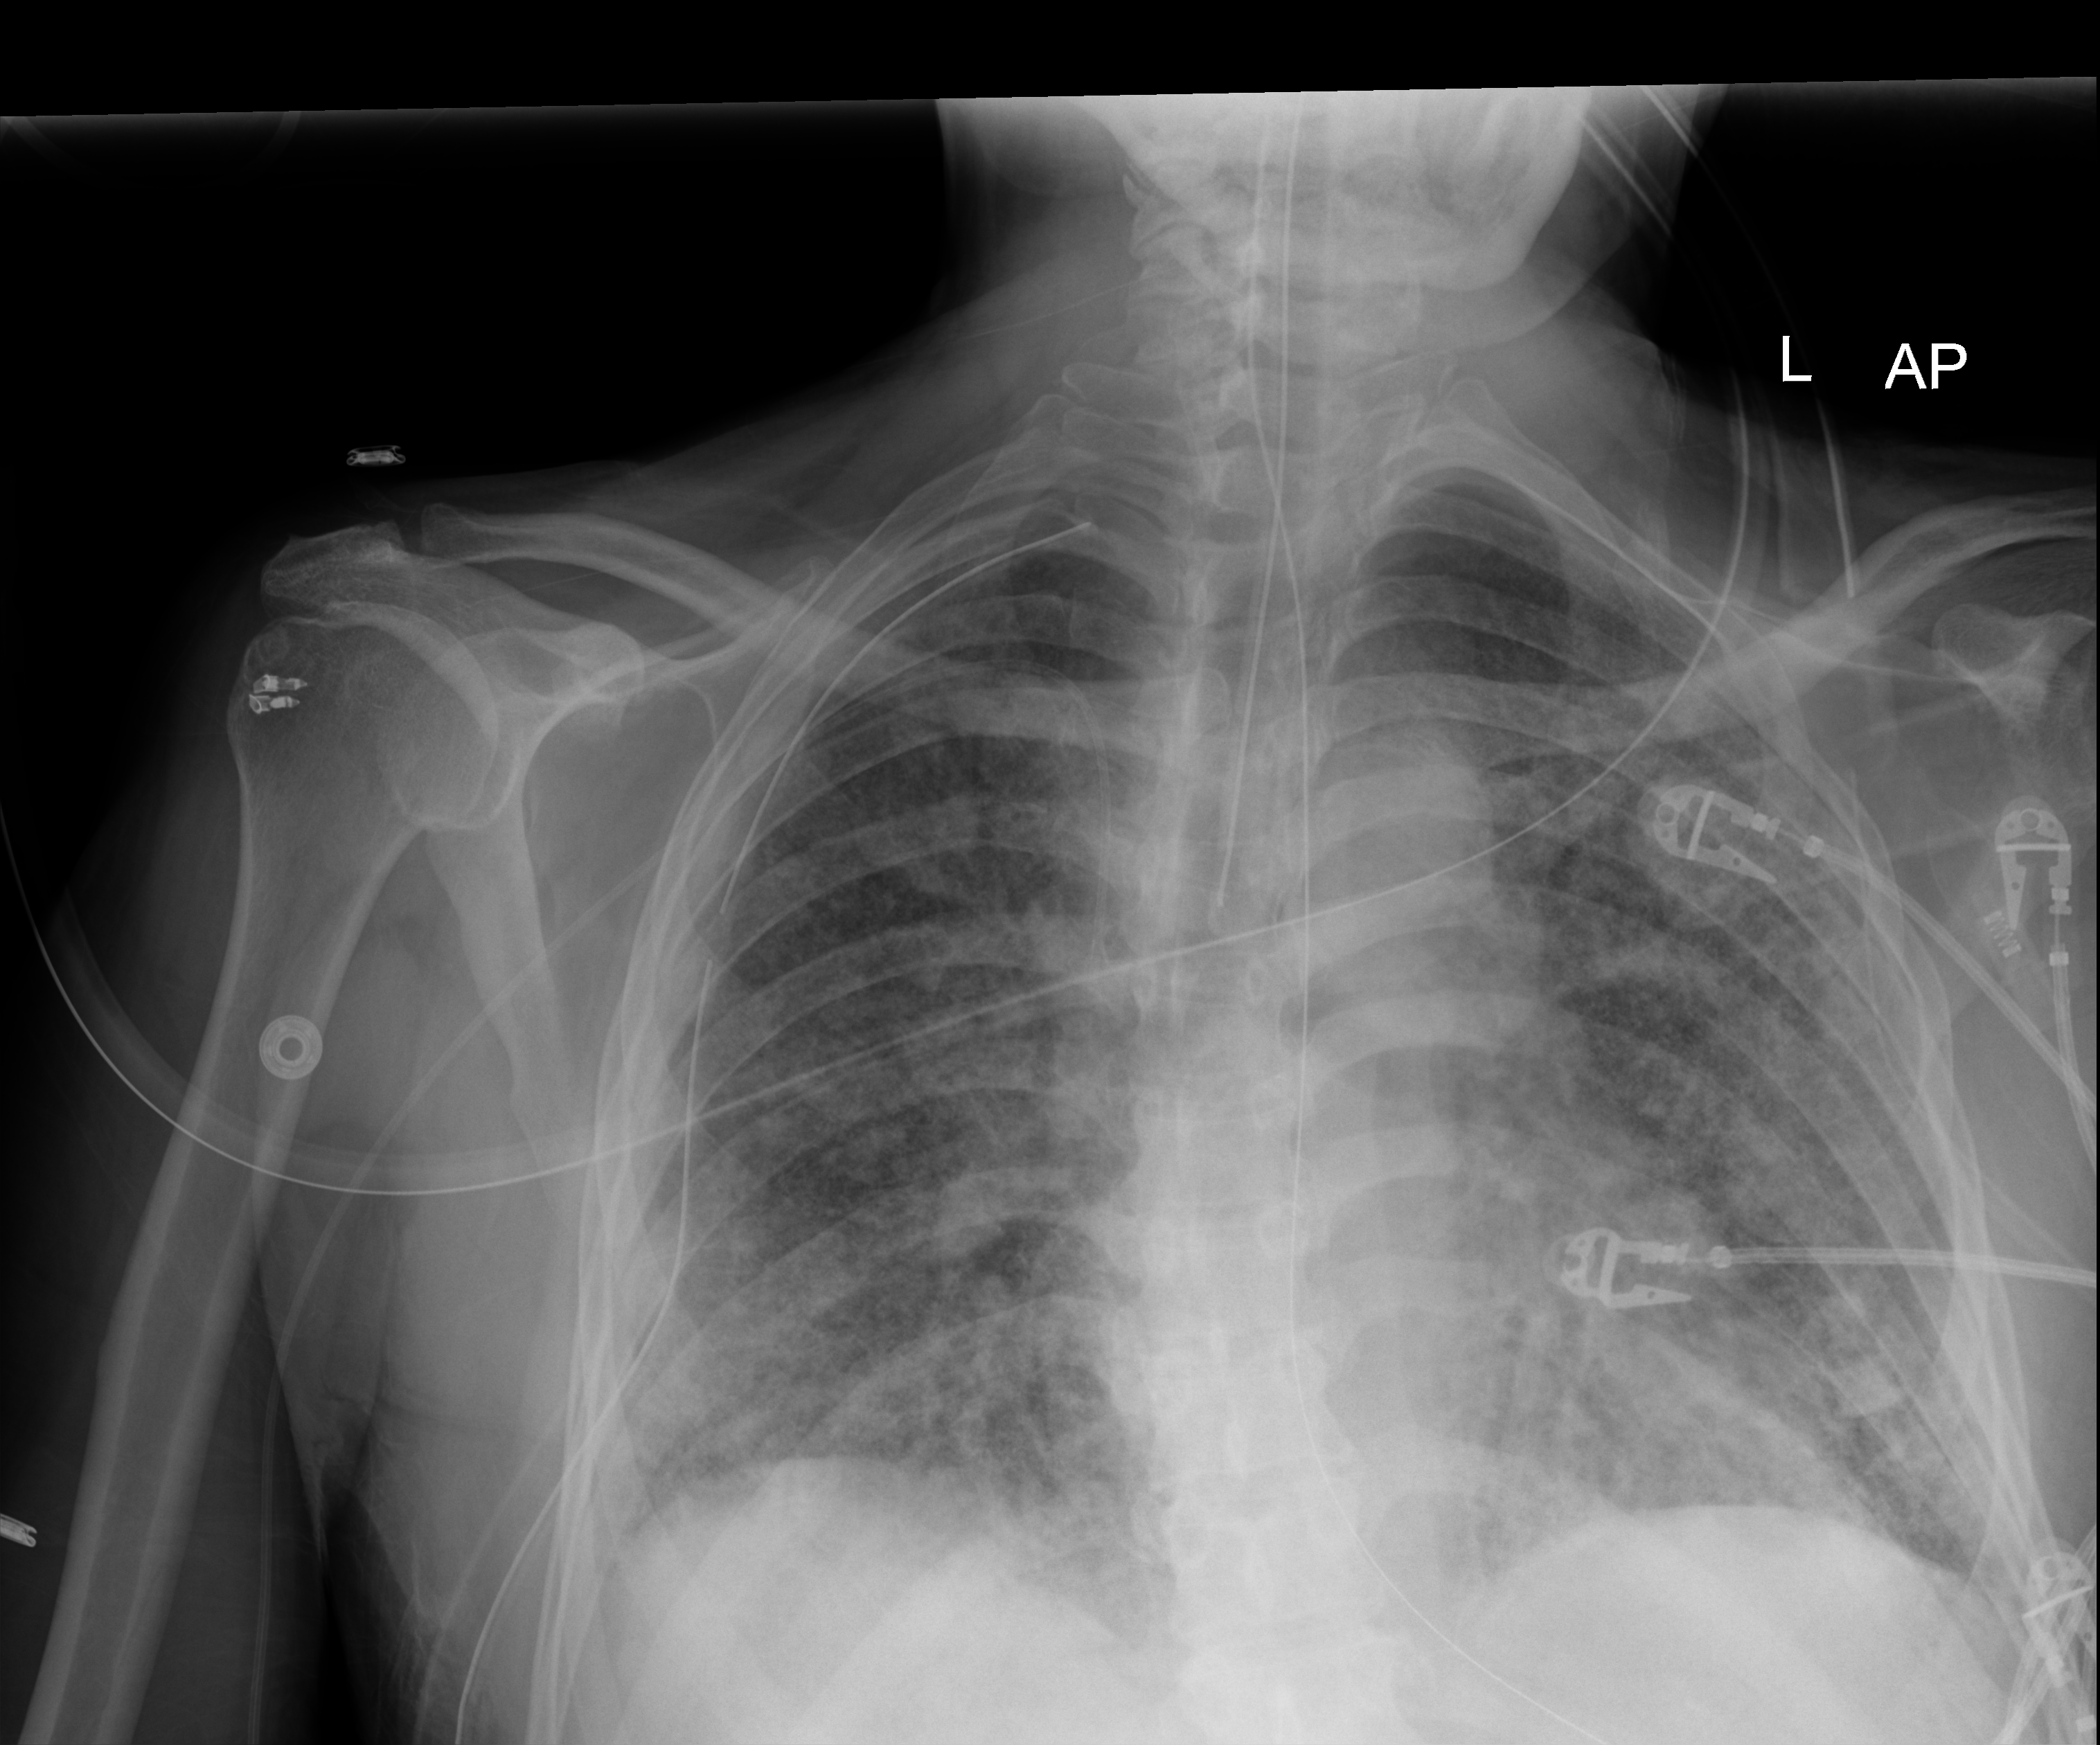
Chest X-ray (portable). Male patient hospitalised with COVID-19, age 60–74 years.
Hospital-stay facts (about this admission, not read from this image; timing relative to this image not recorded): admitted to intensive care during this hospital stay: yes.